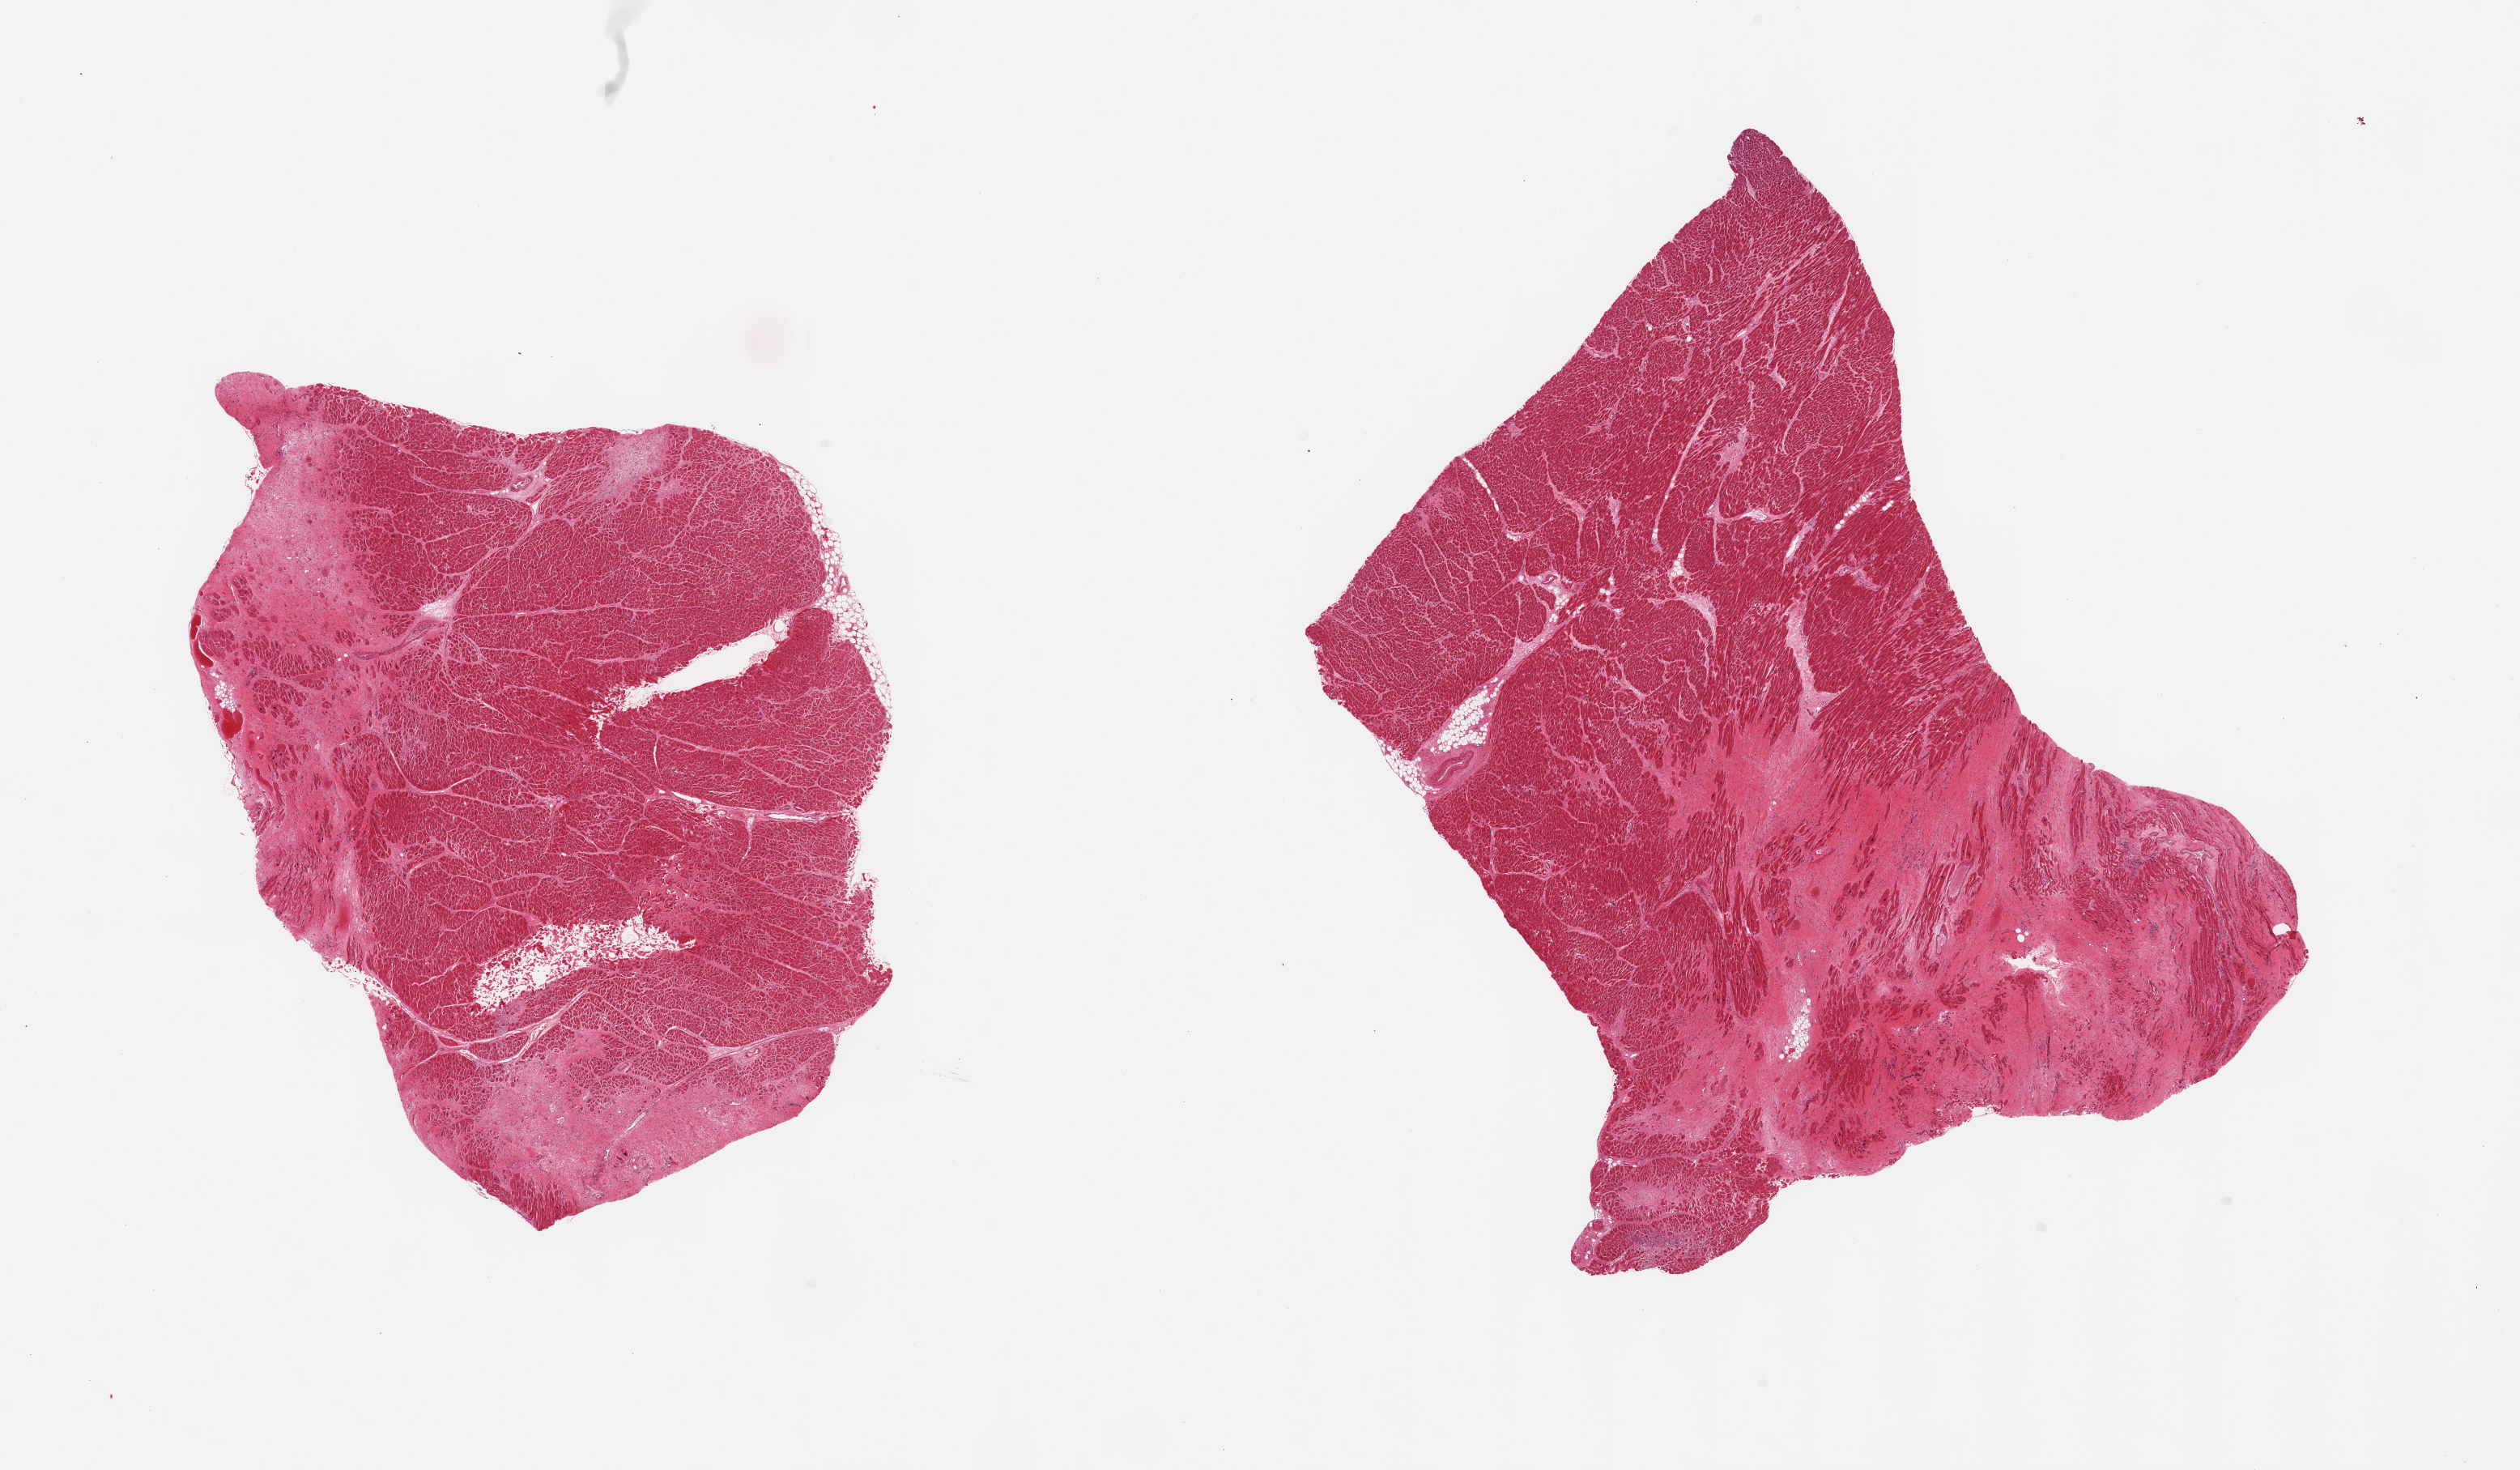
Whole-slide image, H&E stain, brightfield — shown as a low-resolution overview of the whole scanned area (about 24.6 x 14.4 mm); PAXgene-fixed paraffin-embedded (PFPE) section; sampled site (target tissue): heart; tissue donor sample. Donor sex: male.
Review note (as recorded): 2 pieces; extensive [30%] fibrous scars in both pieces, consistent with old 1nfarcts.